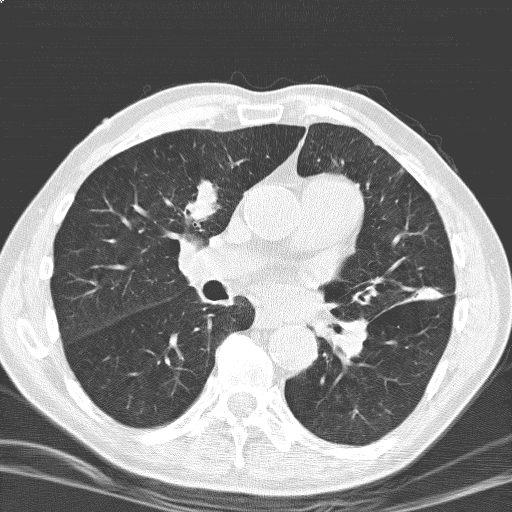
Low-dose screening chest CT, one axial slice; position 99 of 184 along the scan axis; lung window (W 1500 / L -600 HU); 512 × 512 image matrix, field of view 329 × 329 mm.
Outlined on this slice (outlined manually by an expert reader):
- lesion 1 (tumor, upper lobe of right lung): box from (x=187, y=181) to (x=216, y=222) px